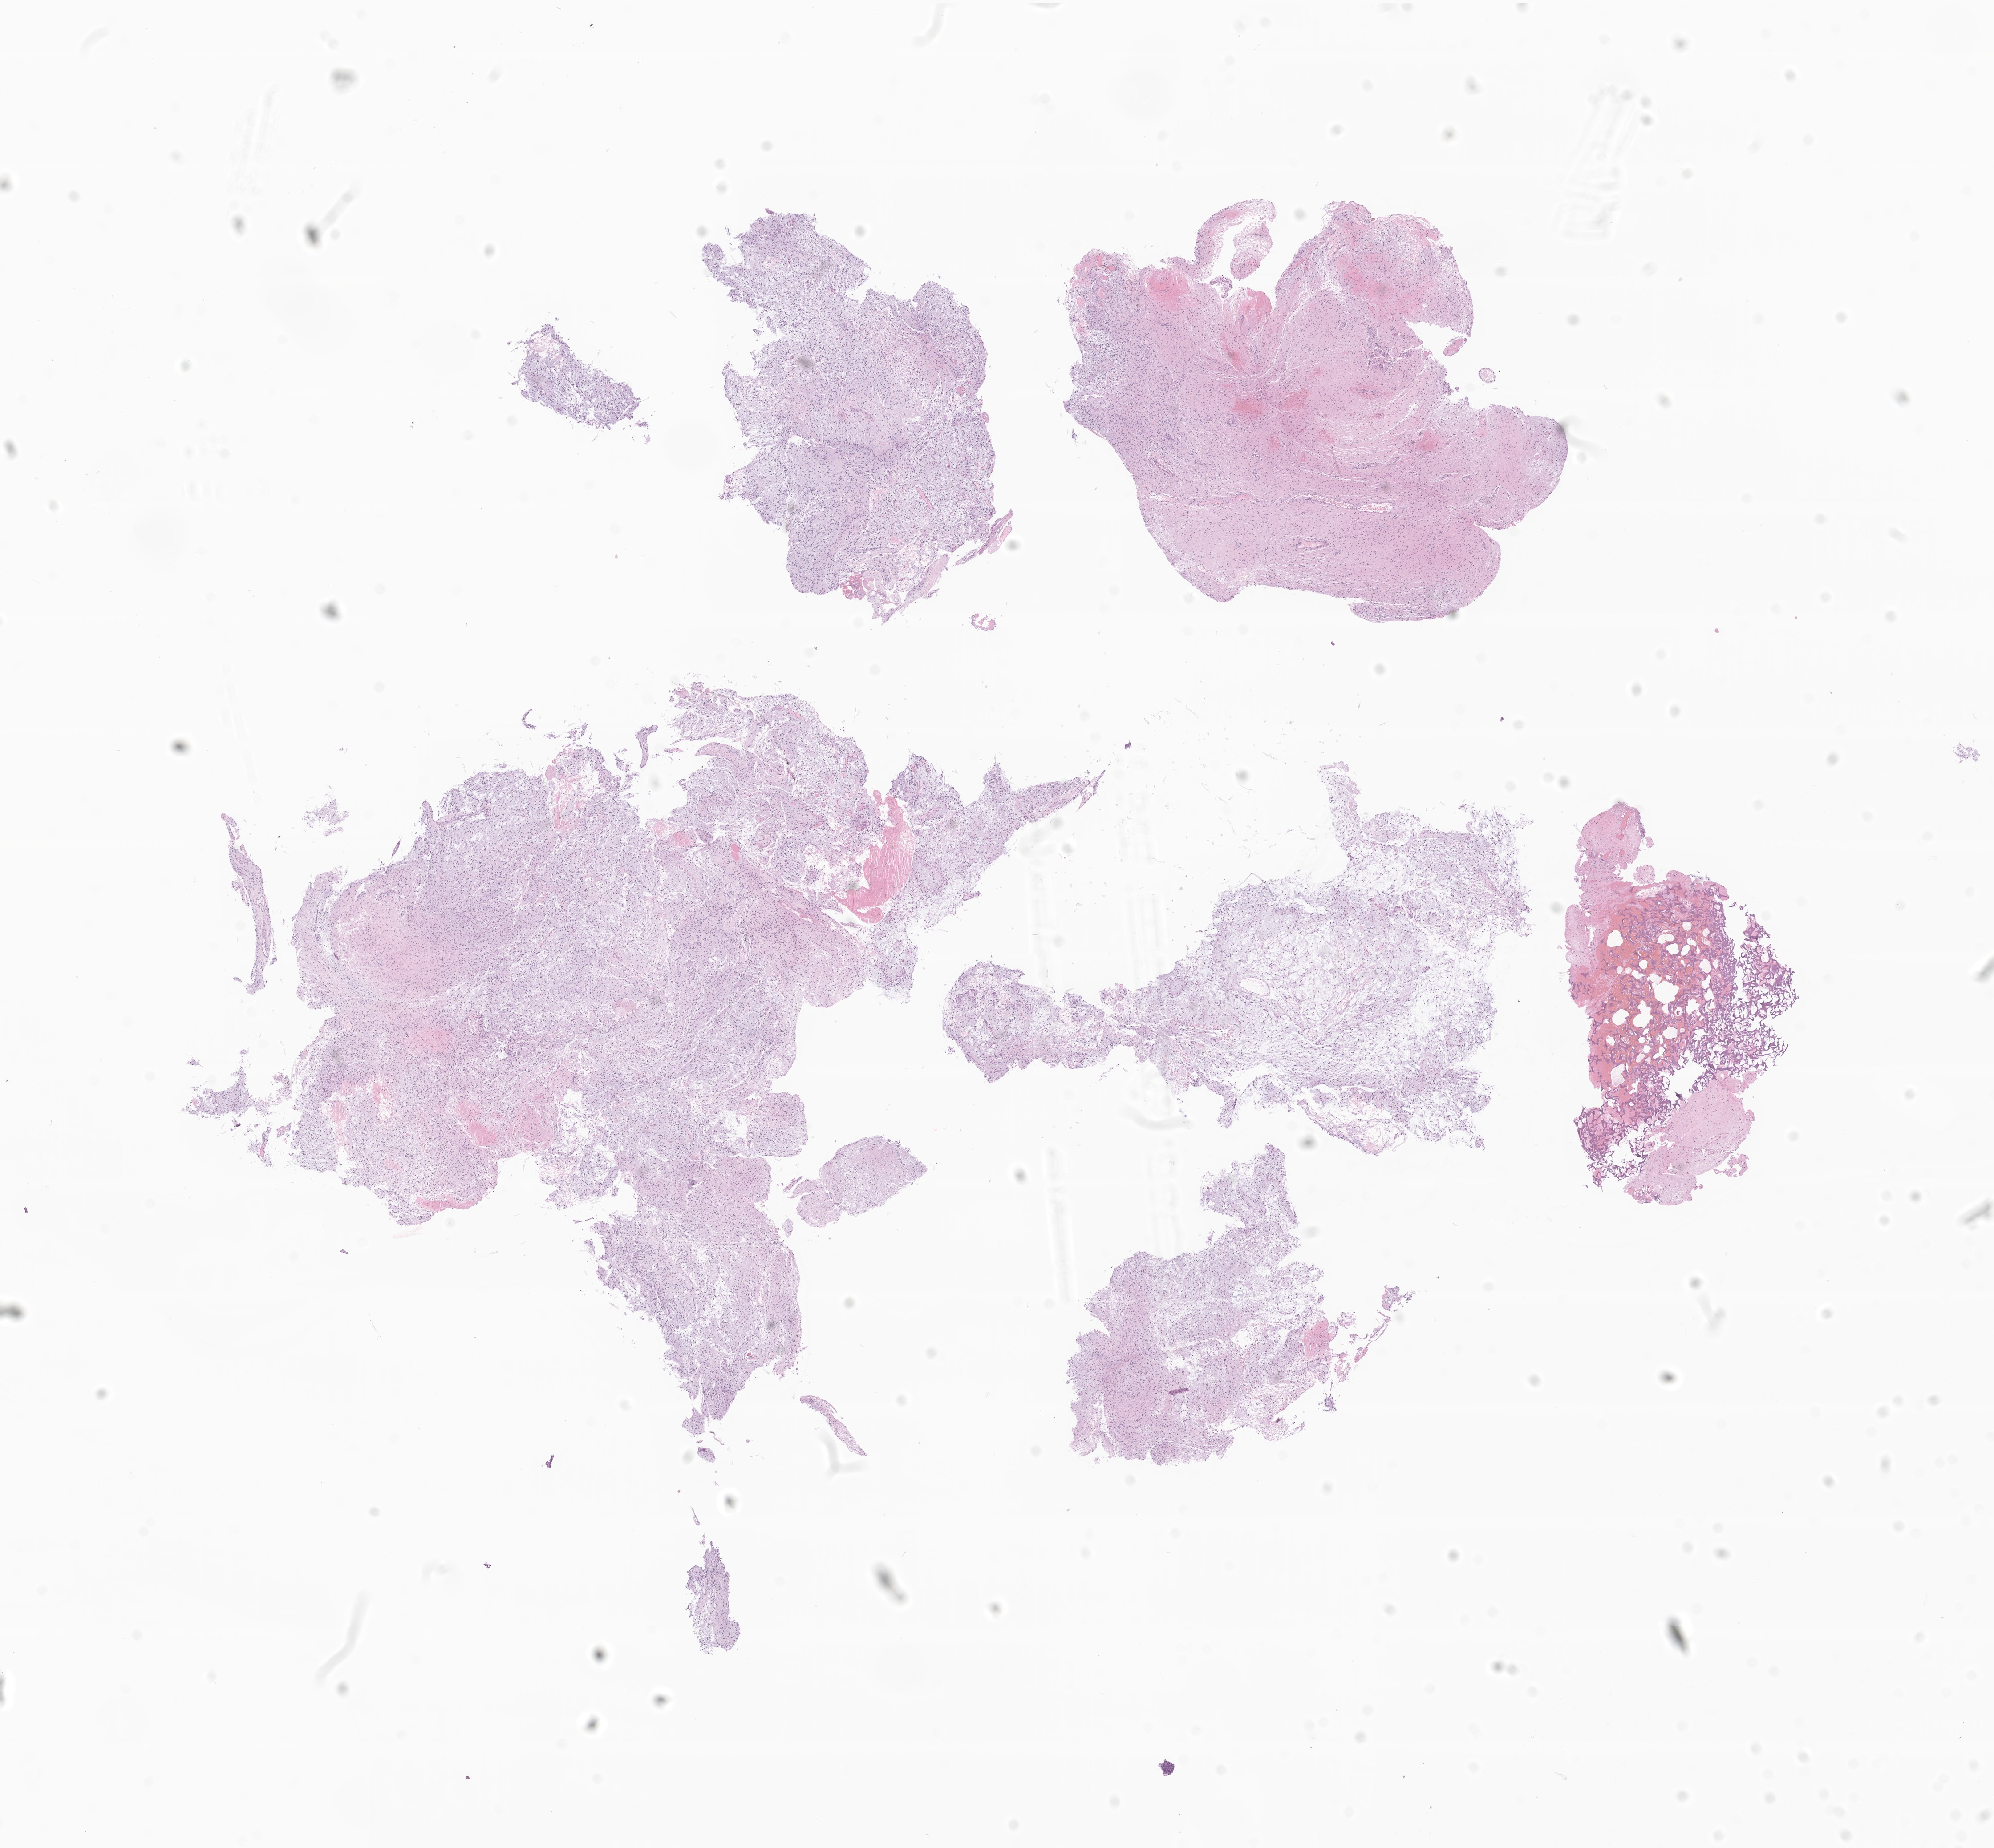
Digitized haematoxylin and eosin-stained section of tumor tissue from the brain stem, whole scanned area (about 18.9 x 17.5 mm) shown as a low-resolution overview; formalin-fixed paraffin-embedded section. Patient: male, age 54 months (4 years 6 months).
- diagnosis (ICD-O-3 morphology term): Pilocytic astrocytoma